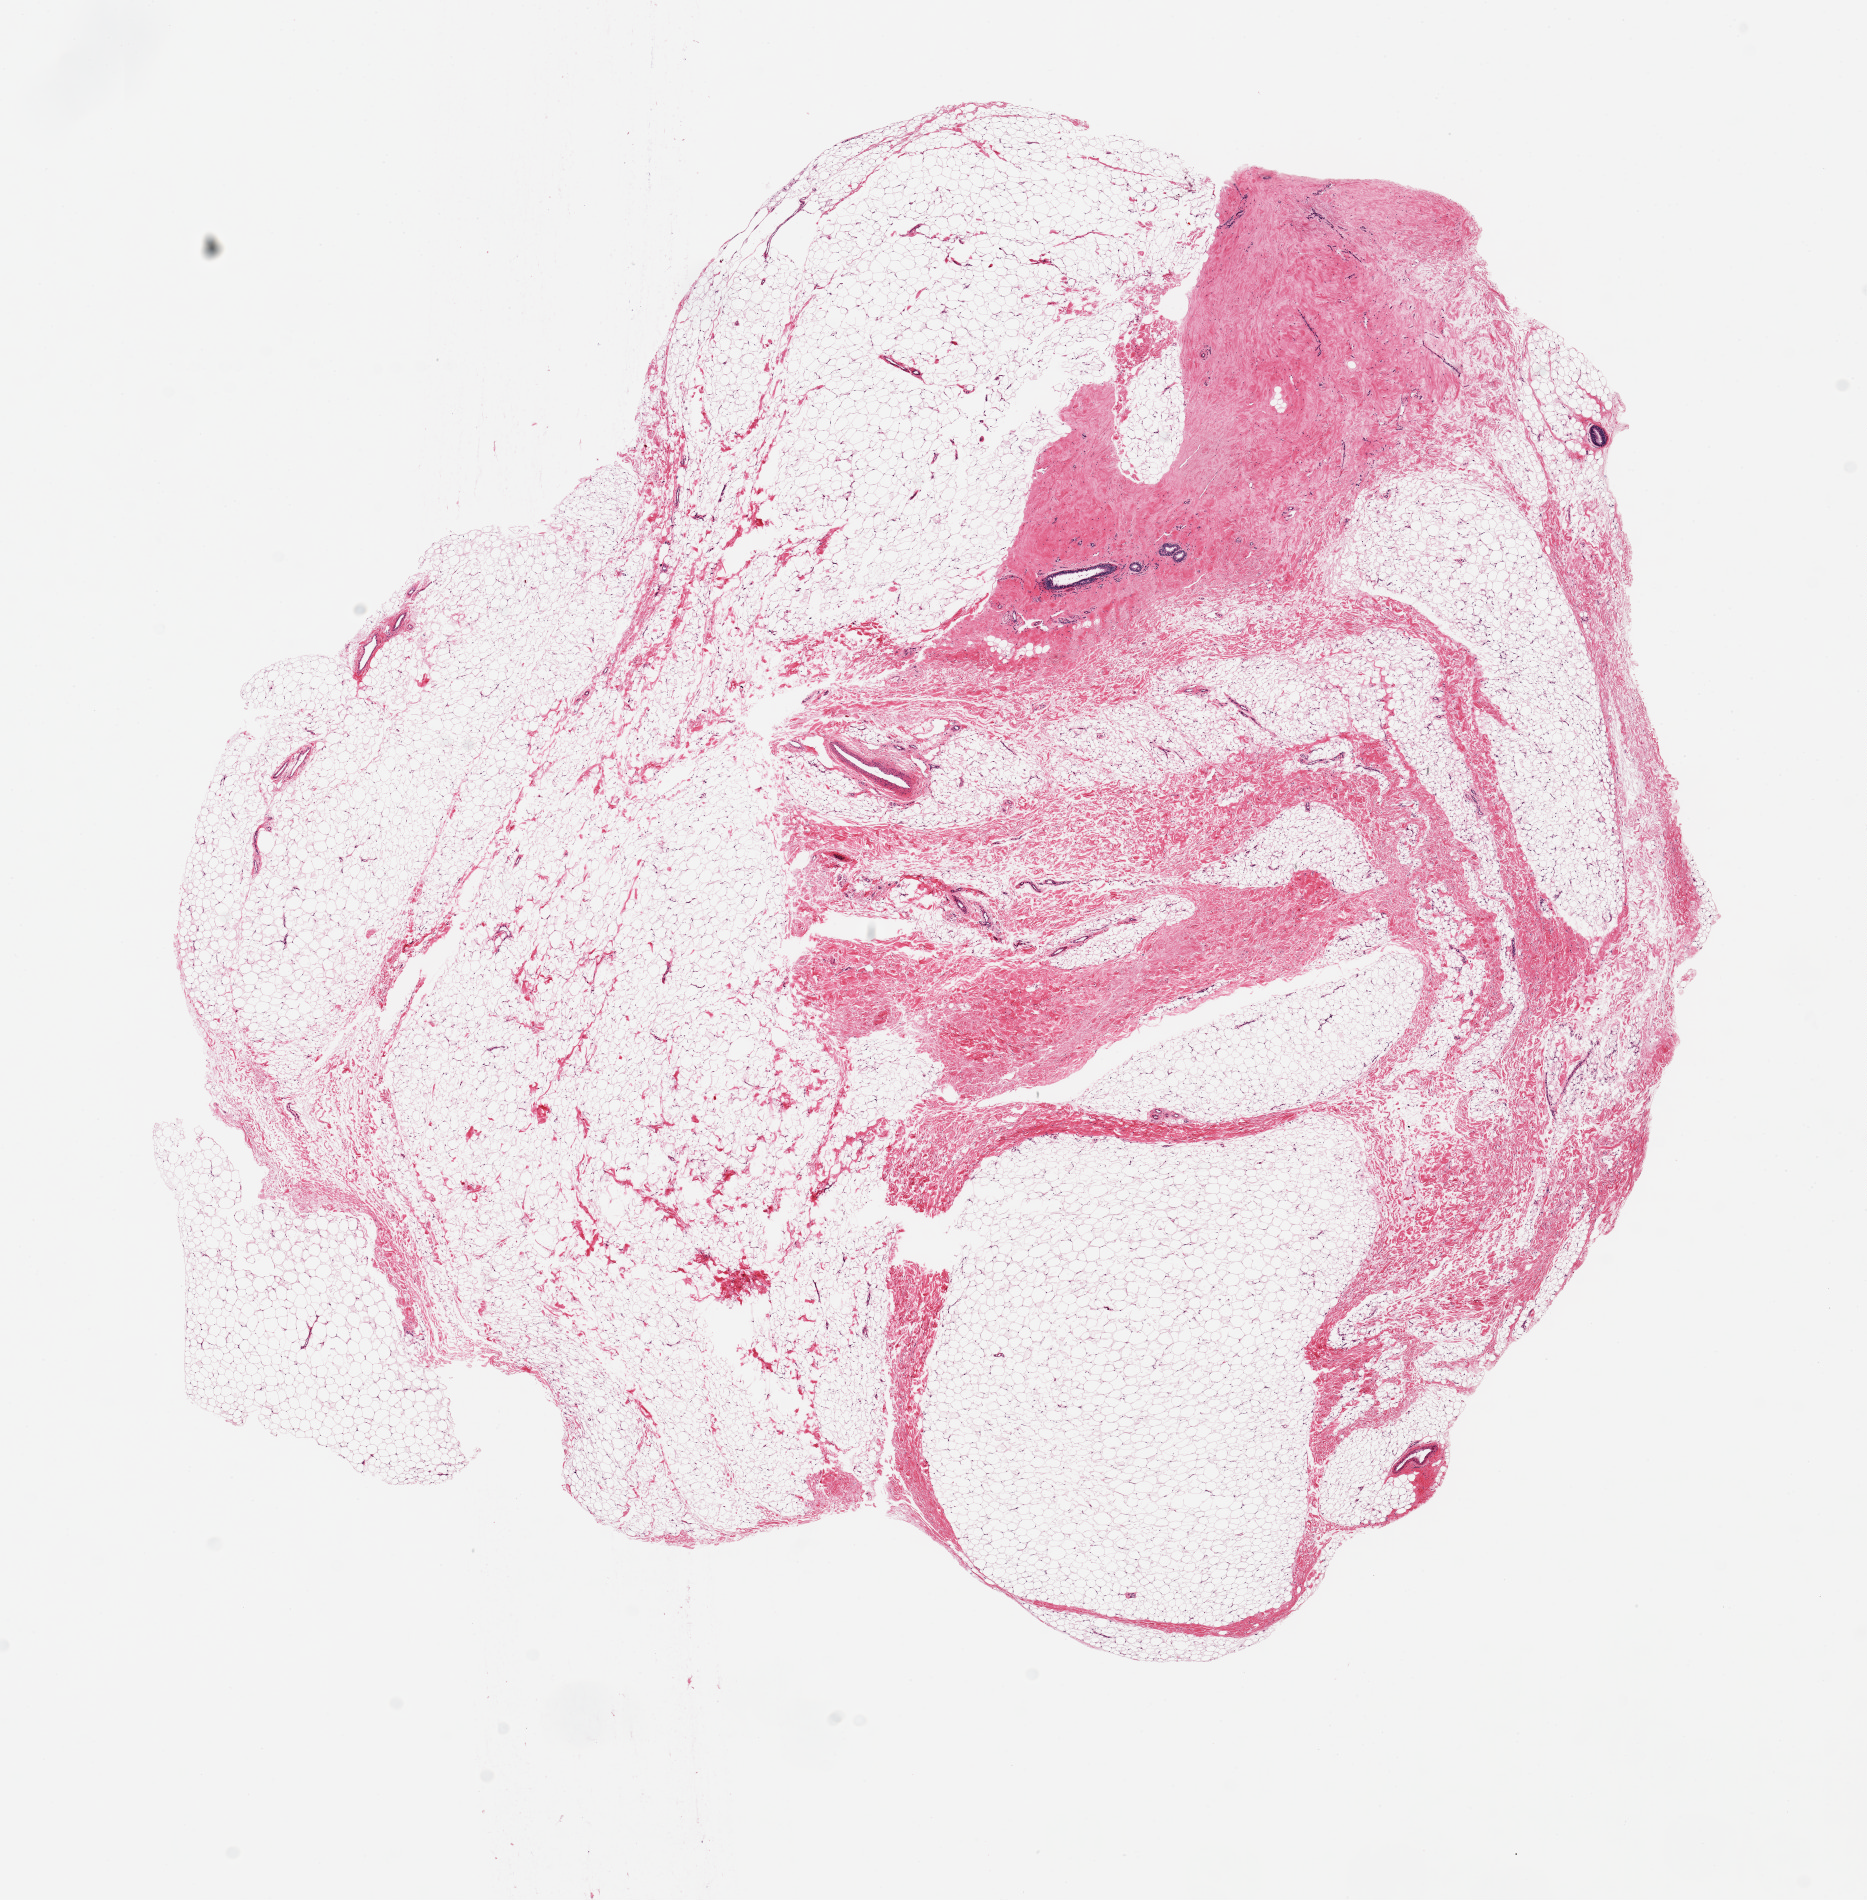
Whole-slide image, H&E stain, brightfield, shown as a low-resolution overview of the whole scanned area (about 14.8 x 15.0 mm). PAXgene-fixed paraffin-embedded (PFPE) section. Sampled site (target tissue): breast. Donor tissue sample. Male donor.
Reviewer comment on this tissue sample: 1 piece ~11x11mm; Single minute focus of ductal elements.